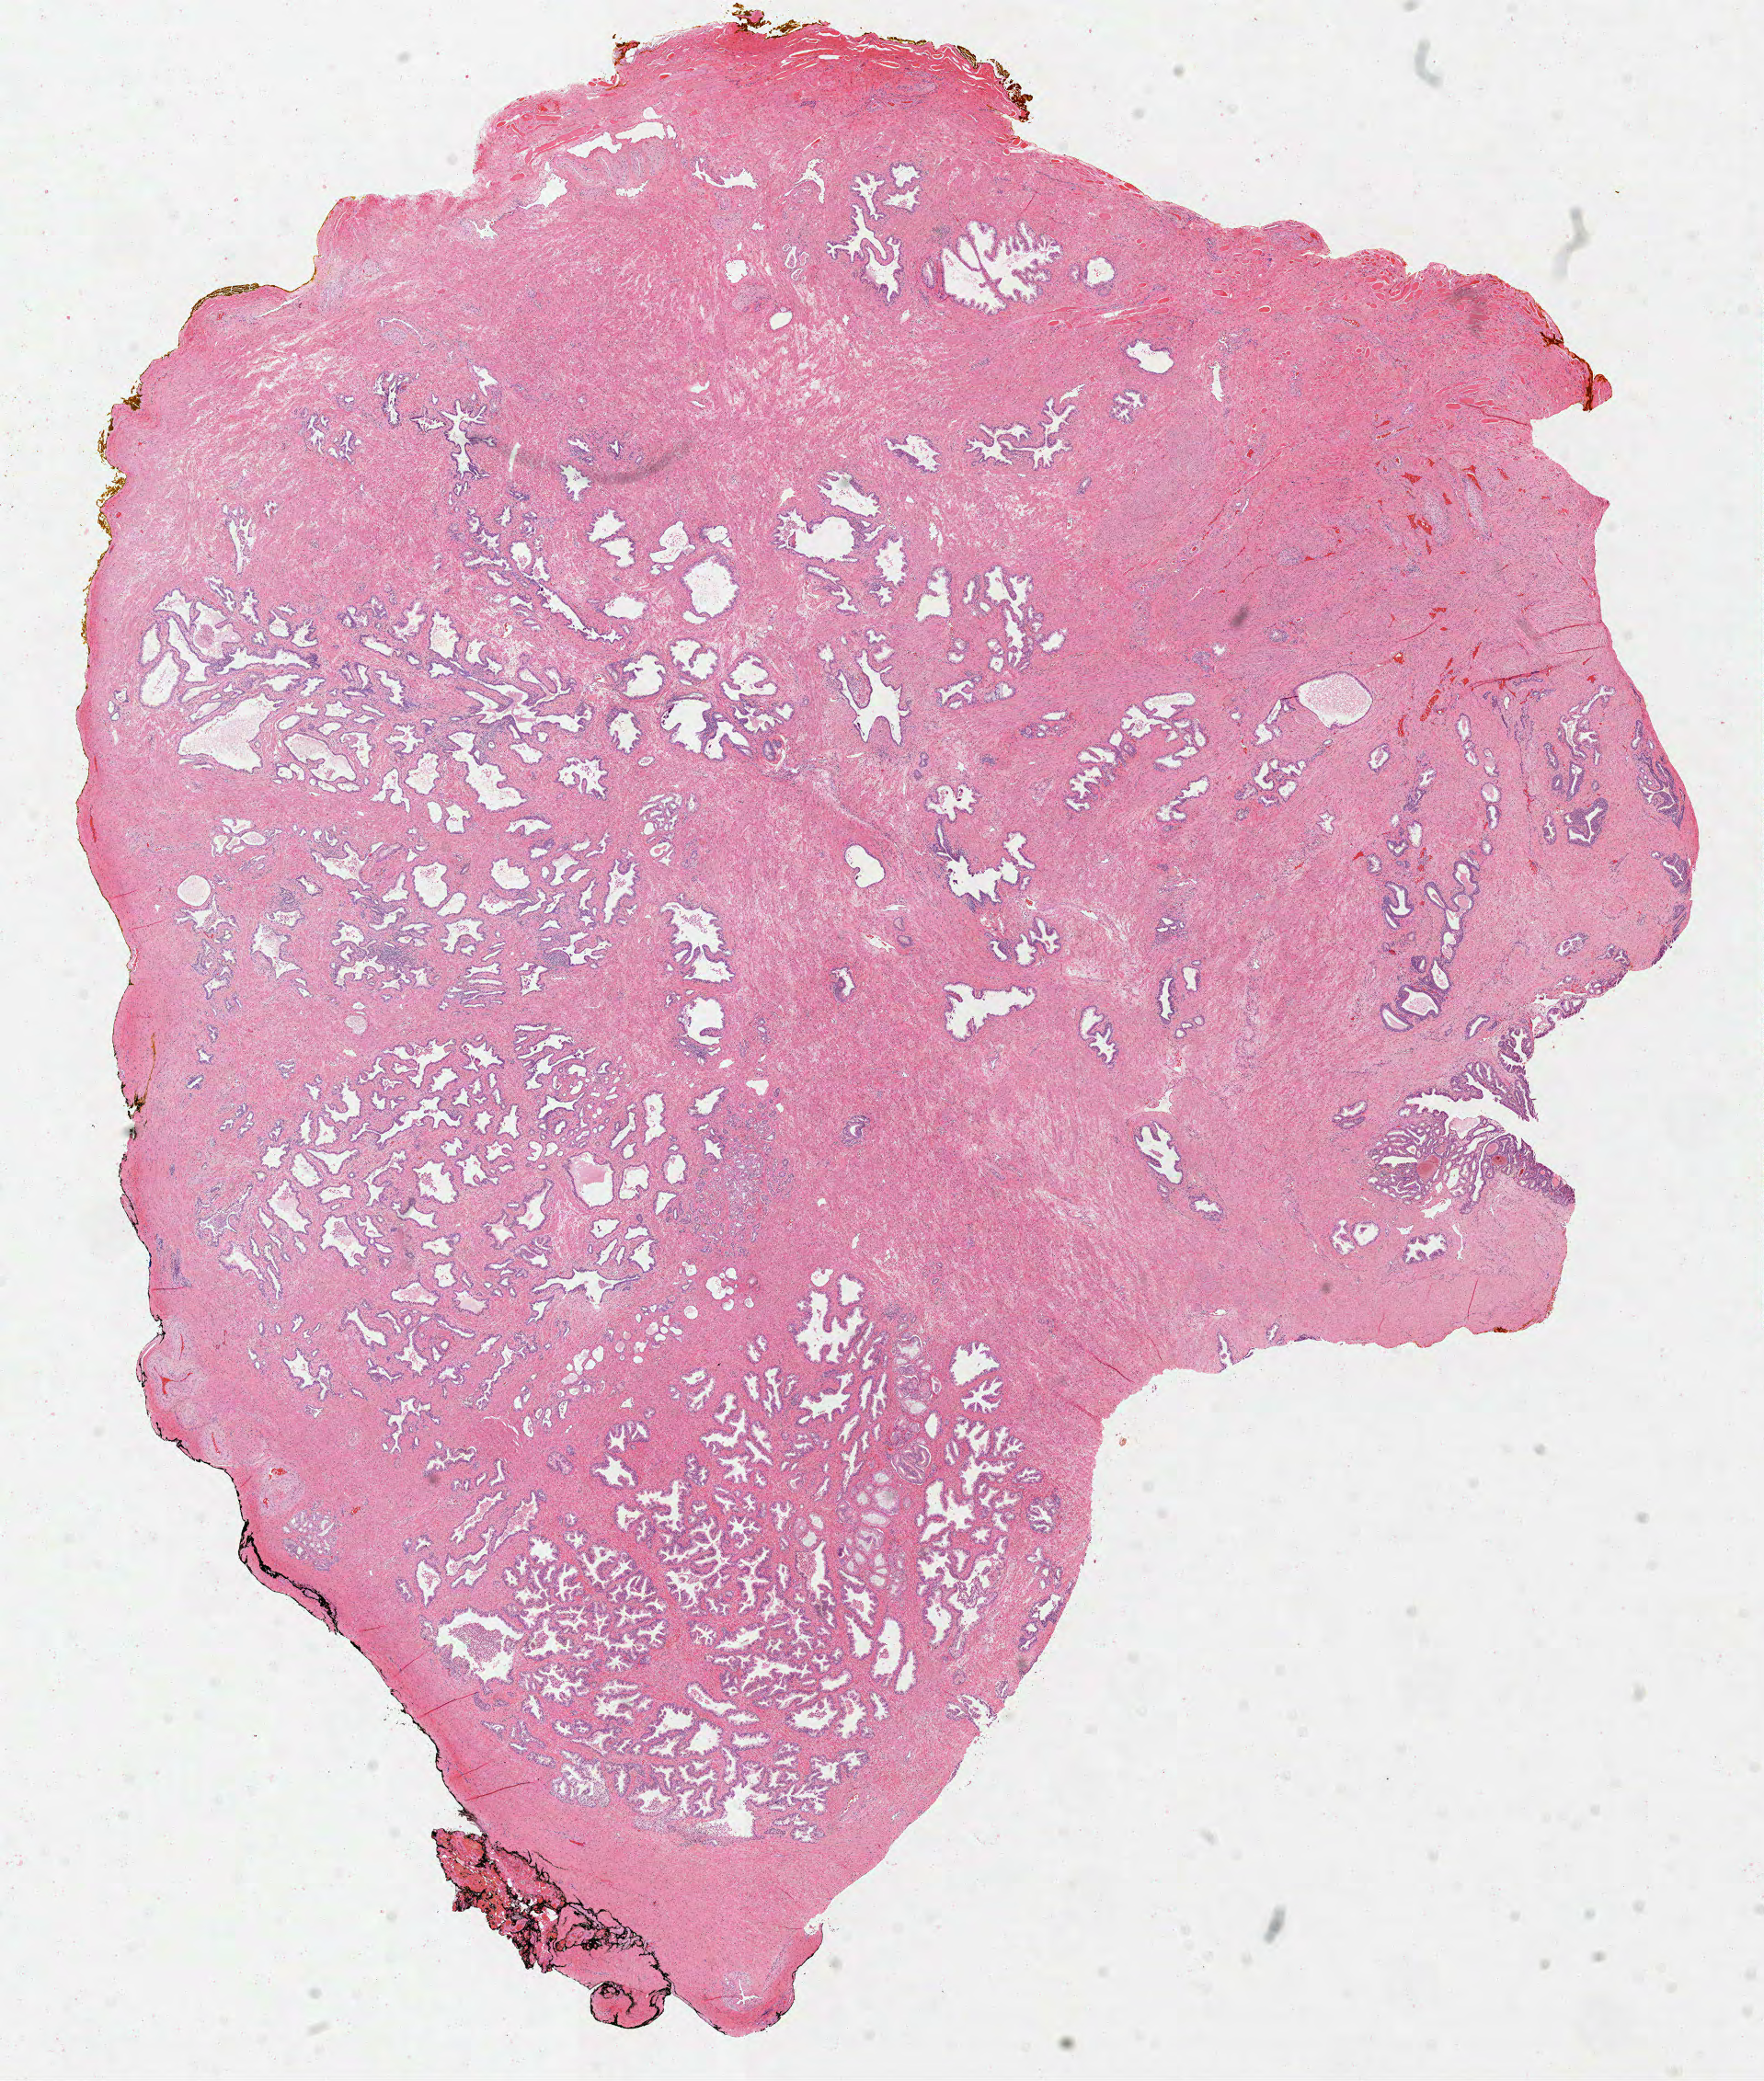
Hematoxylin and eosin (H&E) stained whole-slide image — a low-resolution overview of the entire scanned area, about 15.5 x 18.3 mm; FFPE section; primary tumour sample from the prostate. Male, age 49 years at initial diagnosis. Gleason score: 7 (3+4).
Lymph nodes positive (case pathology): 0 of 9 examined. Laterality: bilateral. Diagnosis: Acinar cell carcinoma (prostate gland).